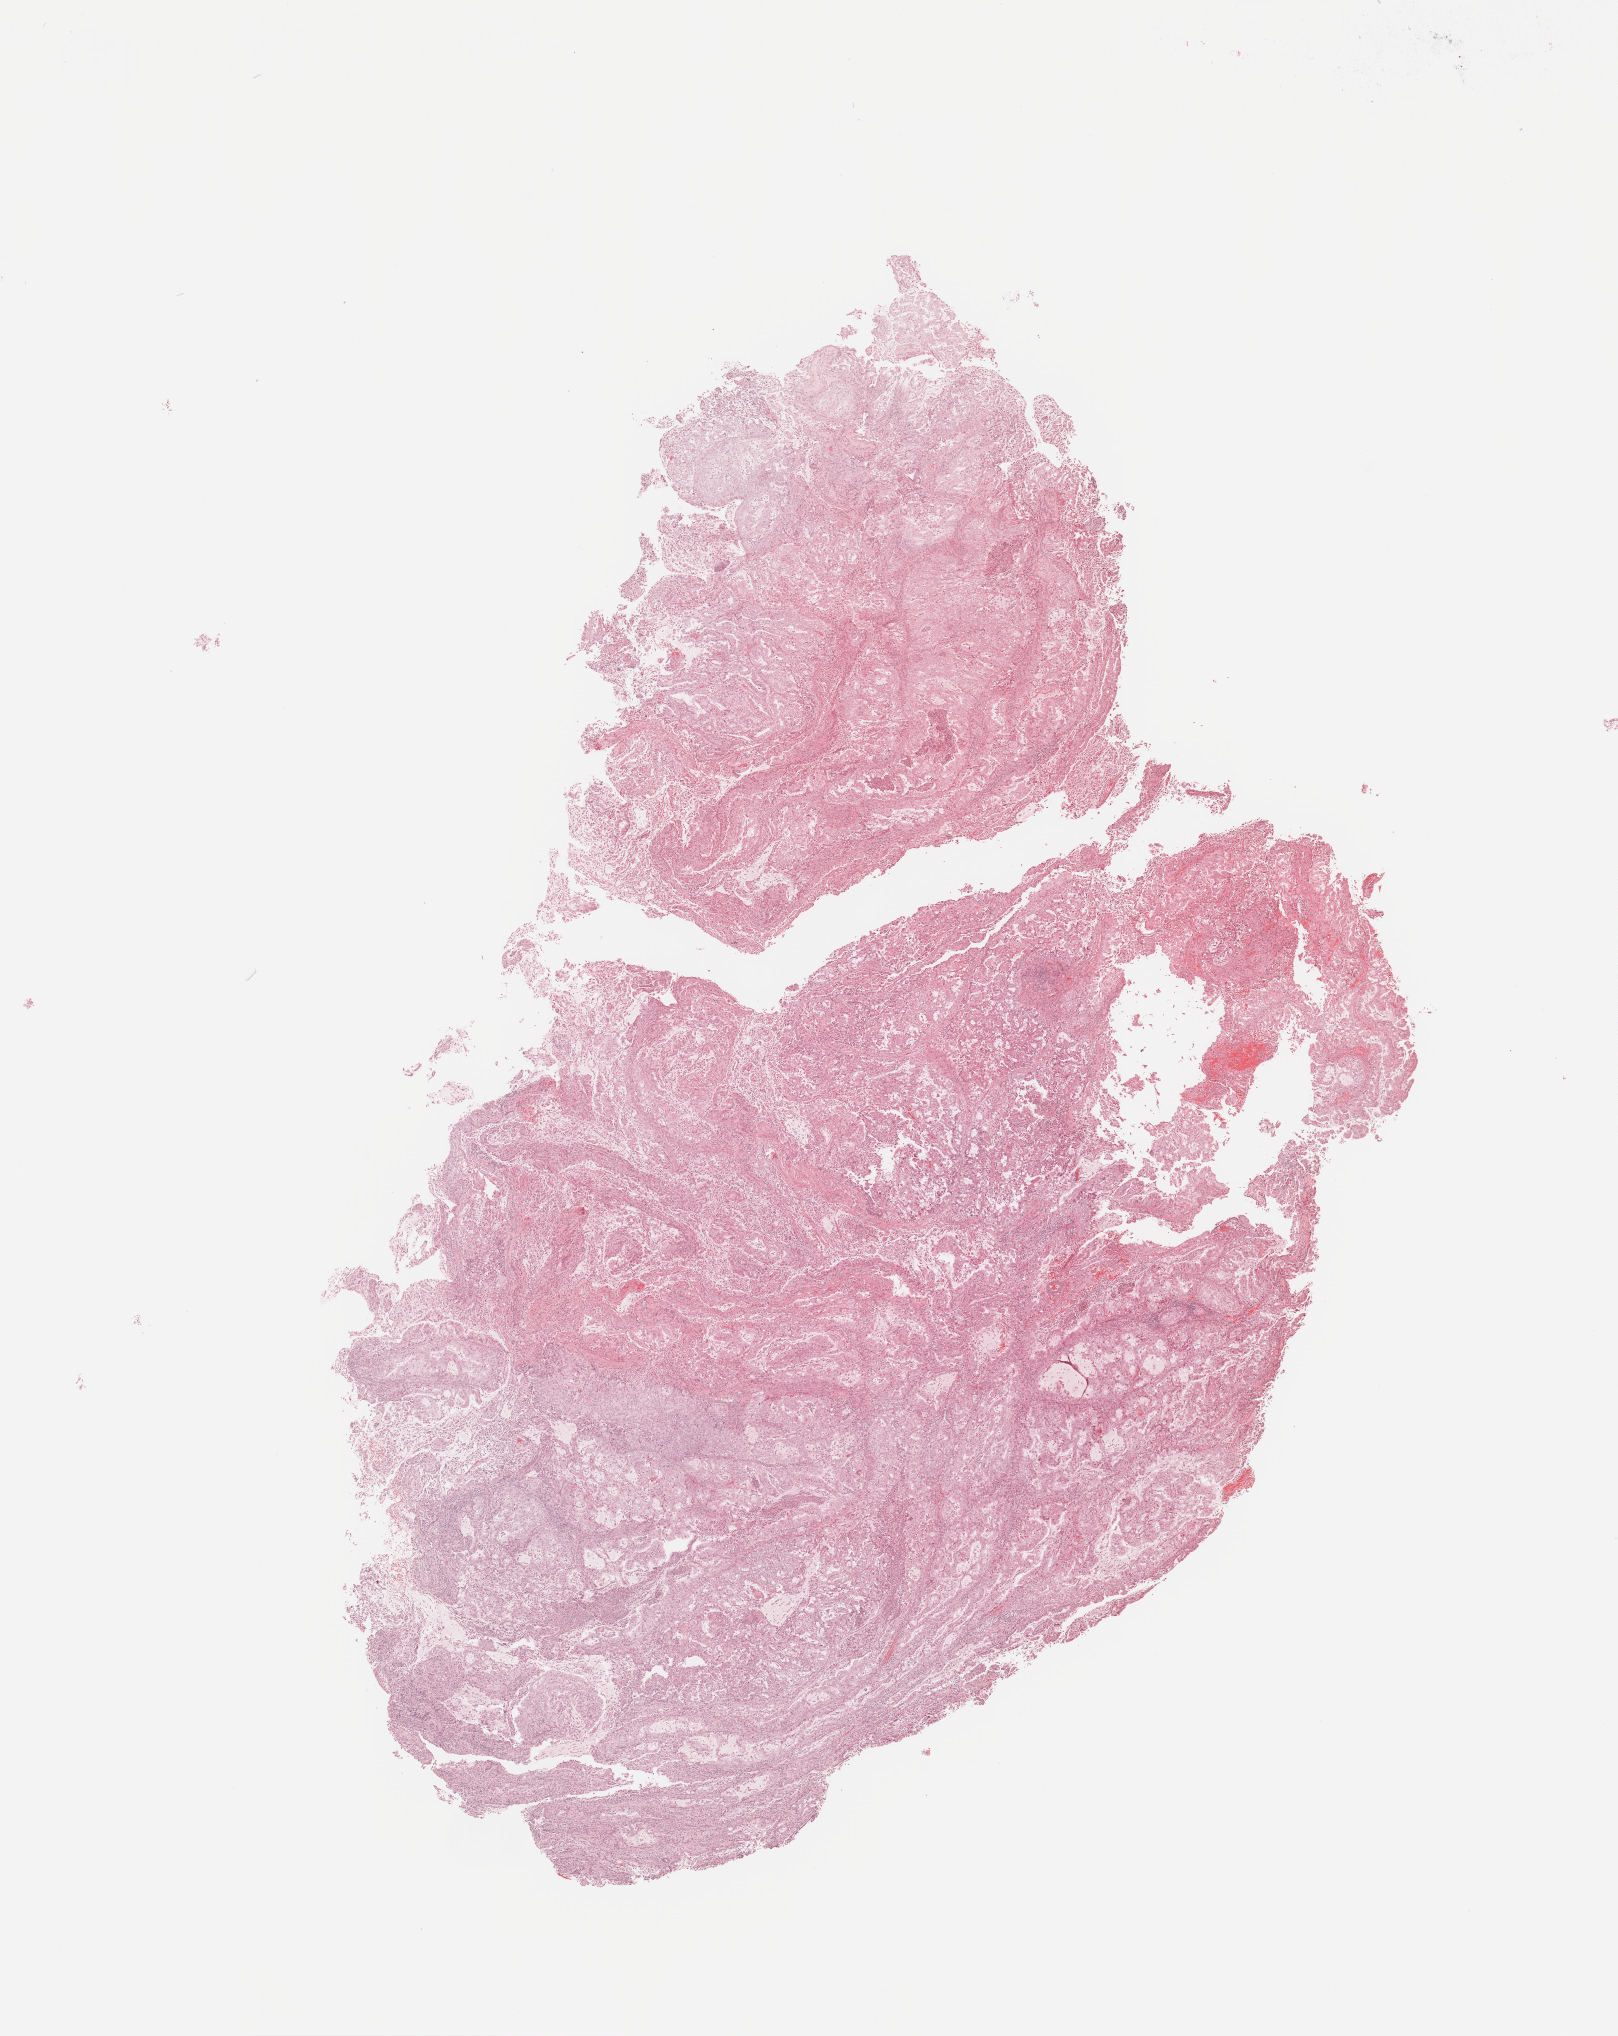
Digitized H&E tissue section (whole slide) — a low-resolution overview of the entire scanned area, about 12.8 x 16.1 mm (acquisition: 20x scan), tumour tissue sample, sampled site: uterus. Patient: female, age 65 years.
Histologic diagnosis: Endometrioid adenocarcinoma, NOS.